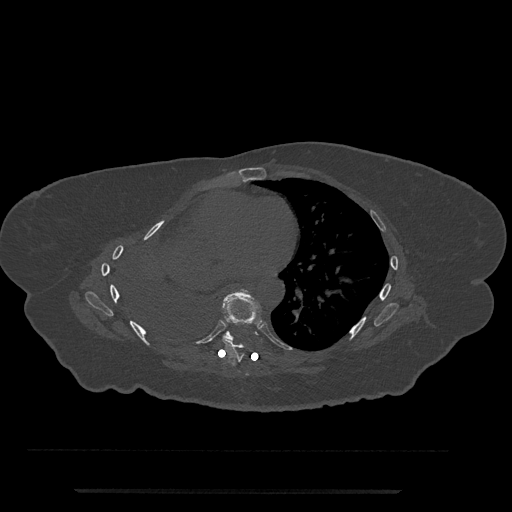
CT including the spine, one axial slice; position 425 of 797 along the scan axis; bone window (W 1800 / L 400 HU); 0.5 mm slice thickness; 512 × 512 image matrix, field of view 440 × 440 mm. Female patient, age 51 years. From the clinical record (not read from this slice): primary cancer: neuro; vertebrae with lytic lesions (as recorded): T8.
Outlined on this slice (semi-automatically segmented with operator editing):
- T7 vertebra: bounding box [x1, y1, x2, y2] px = [222, 289, 263, 362]
- T8 vertebra: [223, 331, 234, 341]